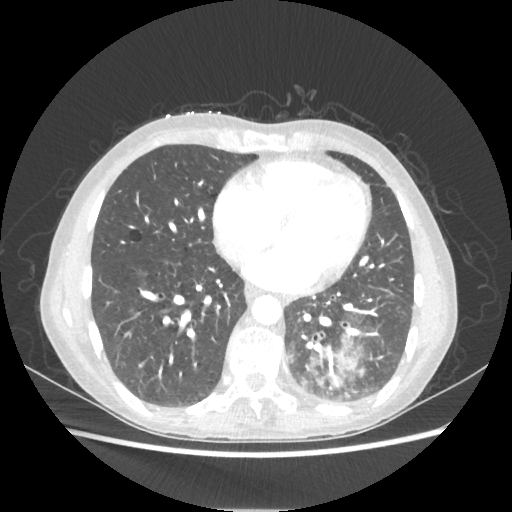
Chest CT, one axial slice; slice 81 of 221 in the series (ordered by position); reconstruction kernel STANDARD; lung window (W 1500 / L -600 HU); 512 × 512 image matrix, field of view 360 × 360 mm. Female patient, age 53 years. From the clinical record (not read from this slice): clinical TNM (as recorded): T3 N0 M0.
Annotated regions visible in this slice (rectangle marked by the reading radiologist):
- lung tumour (recorded histology: adenocarcinoma): box from (x=310, y=346) to (x=358, y=375) px